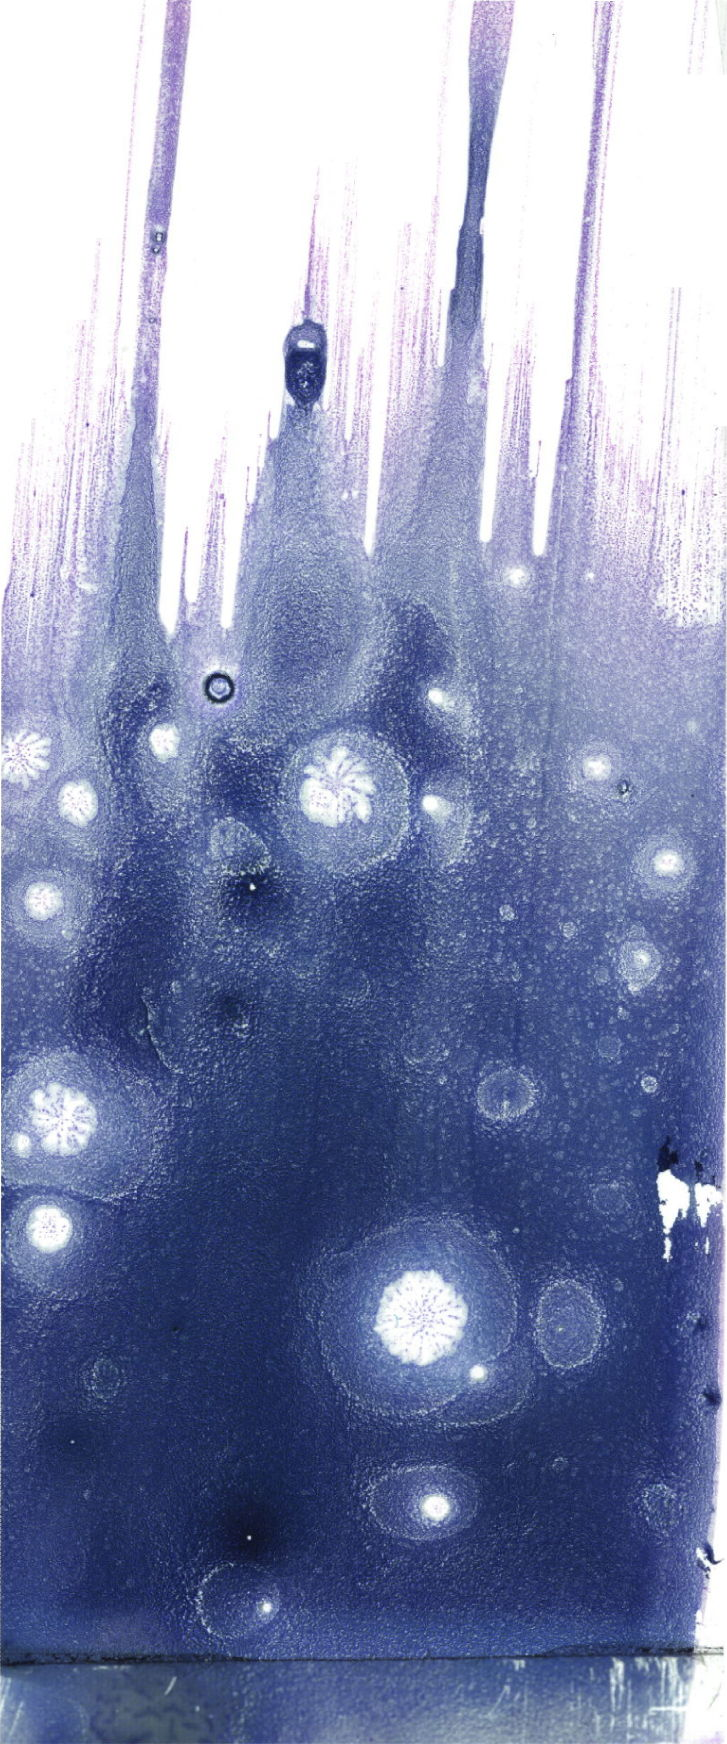
Whole-slide image of a May-Grünwald-Giemsa (MGG)-stained bone marrow aspirate smear — whole scanned area (about 20.6 x 49.4 mm) shown as a low-resolution overview. Female patient.
Diagnosis: B Acute Lymphoblastic Leukemia.